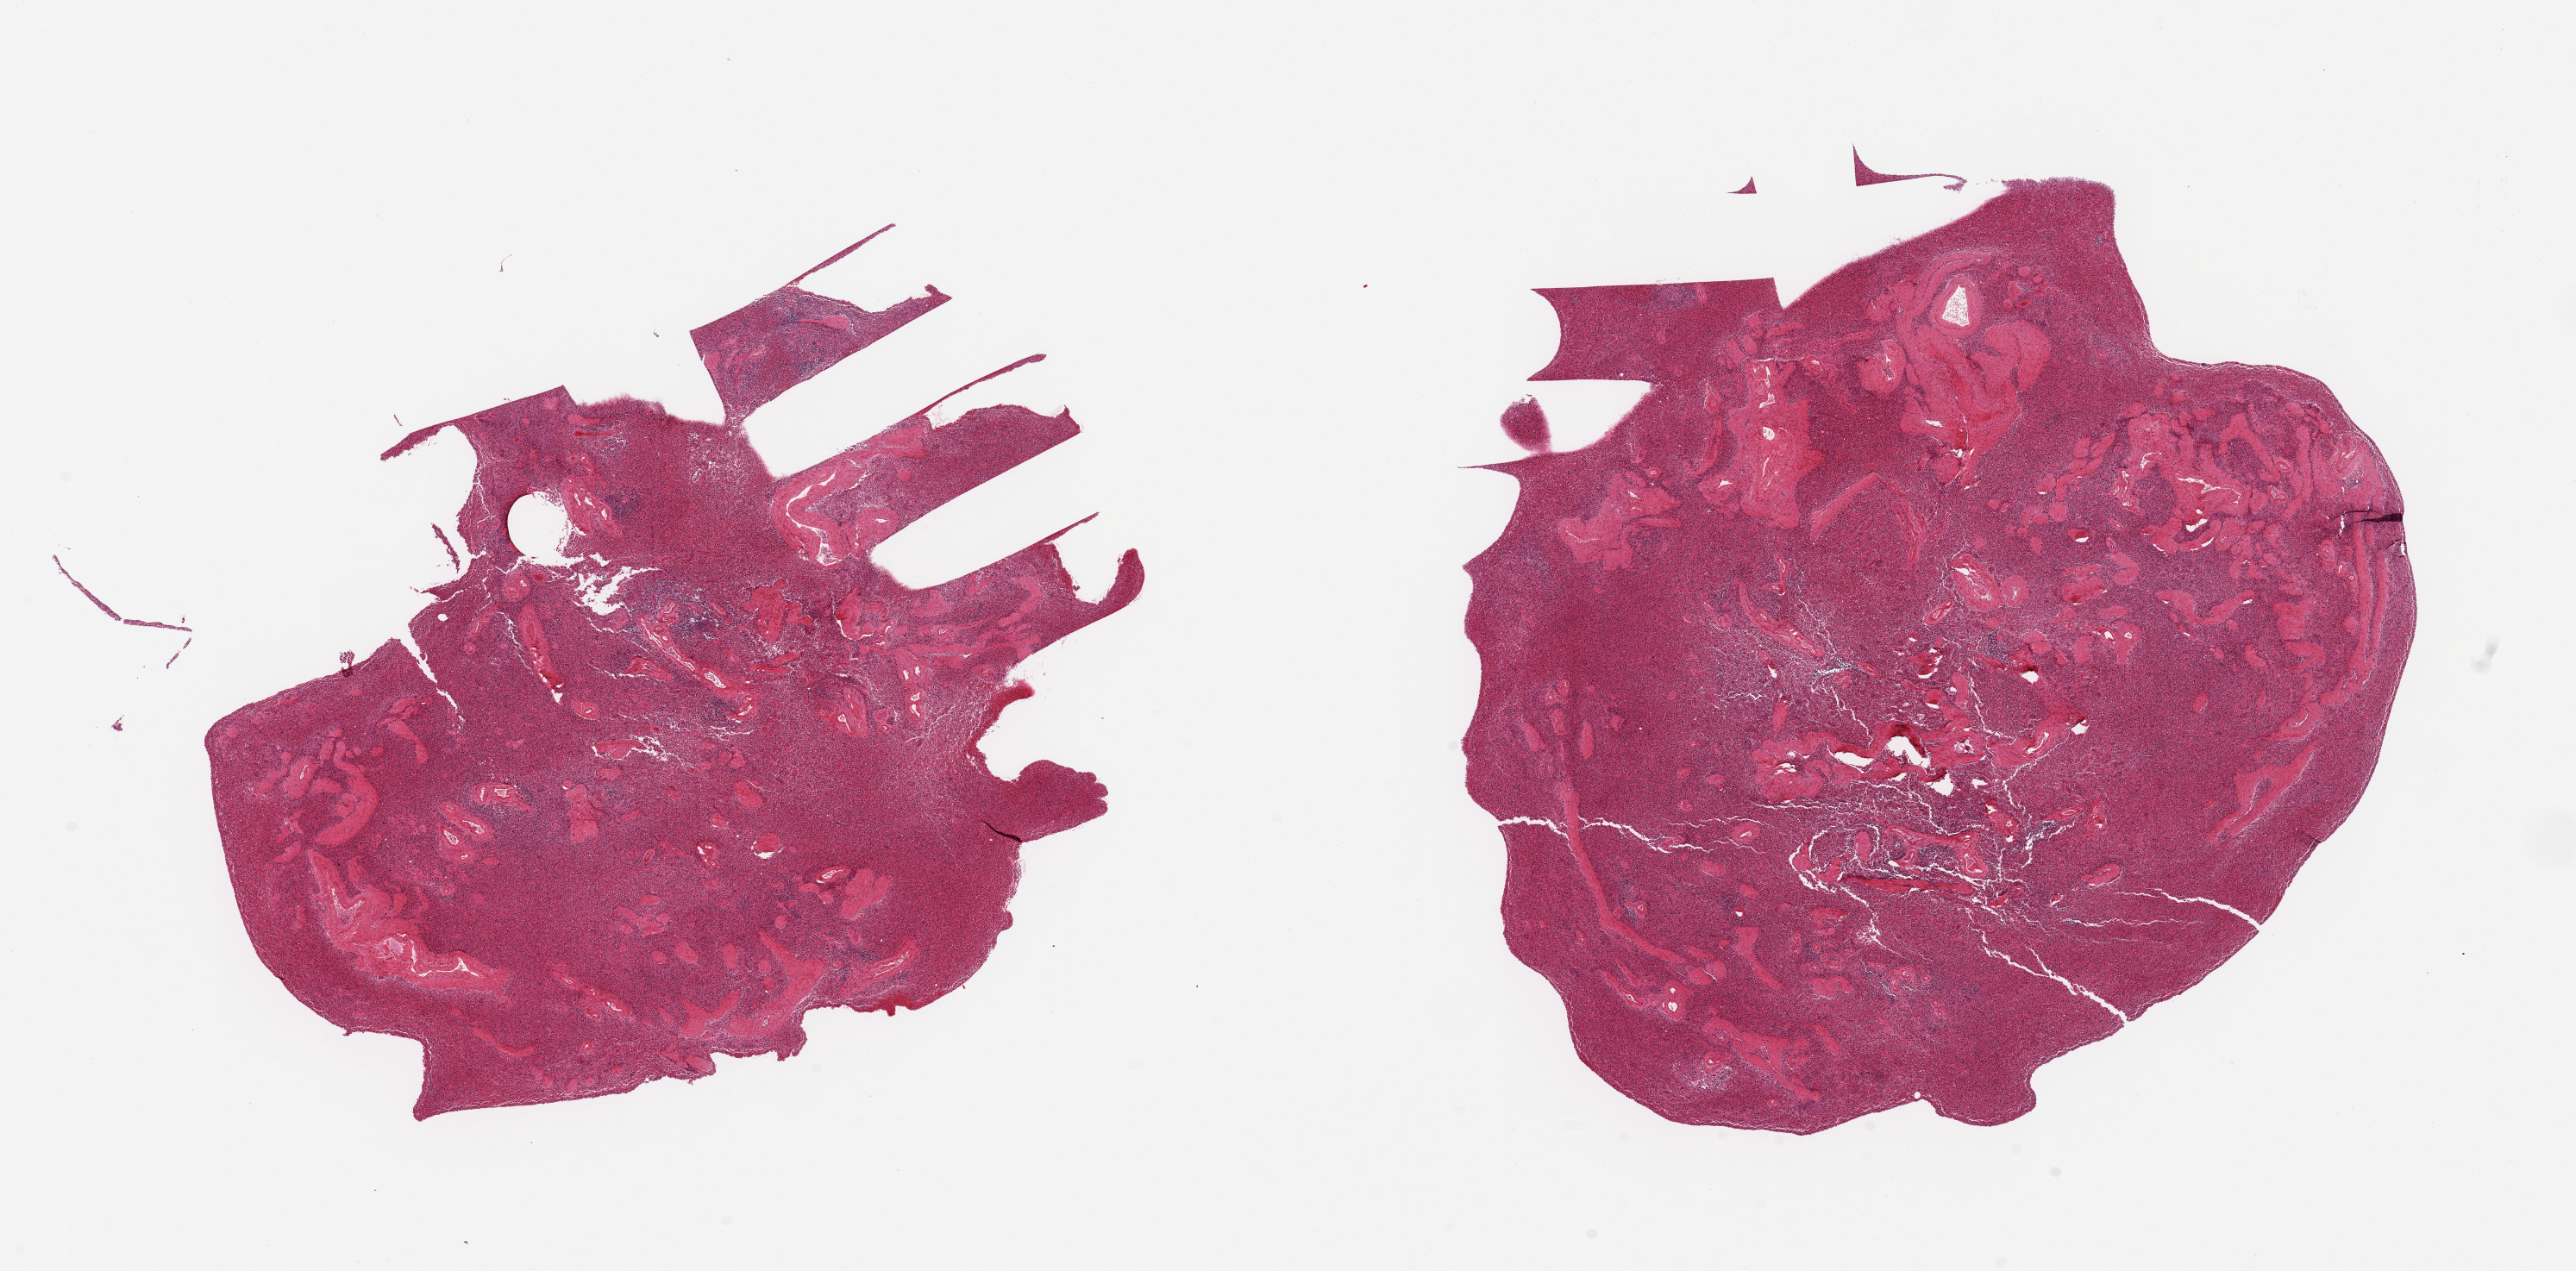
Digitized H&E-stained section, brightfield — low-resolution overview of the scanned area, about 23.6 x 11.7 mm (slide scanned at 20x), PAXgene-fixed paraffin-embedded (PFPE) section, section of spleen (target tissue), tissue donor sample.
Pathologist's review note for this sample: 2 pieces; slight congestion.